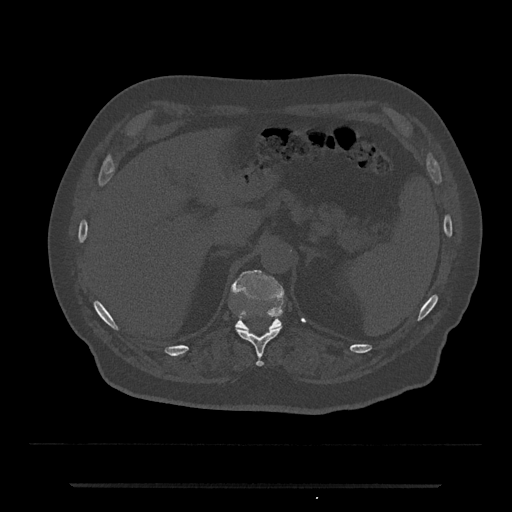
CT including the spine, one axial slice; position 628 of 797 along the scan axis; reconstruction kernel Br40s/3; bone window (W 1800 / L 400 HU); 0.5 mm slice thickness; 512 × 512 image matrix. Male patient, age 80 years. From the clinical record (not read from this slice): primary cancer: prostate; vertebrae with lytic lesions (as recorded): L1, T11.
Structures marked on this image (semi-automatically segmented with operator editing):
- T11 vertebra: bounding box [x1, y1, x2, y2] px = [237, 327, 281, 367]
- T12 vertebra: [231, 269, 285, 331]